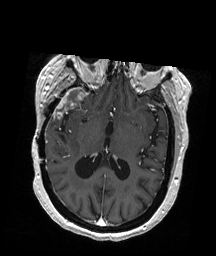
Brain MRI from a brain-tumour surgery series, one axial slice. Slice 101 of 192 in the series (ordered by position). T1-weighted post-contrast. 216 × 256 image matrix, field of view 211 × 250 mm. From the clinical record (not read from this slice): histopathology: Glioblastoma; WHO grade: 4; IDH mutation: no.
Structures marked on this image (manually delineated by an expert):
- tumour: bounding box (x1, y1, x2, y2) in pixels: (56, 87, 86, 115)